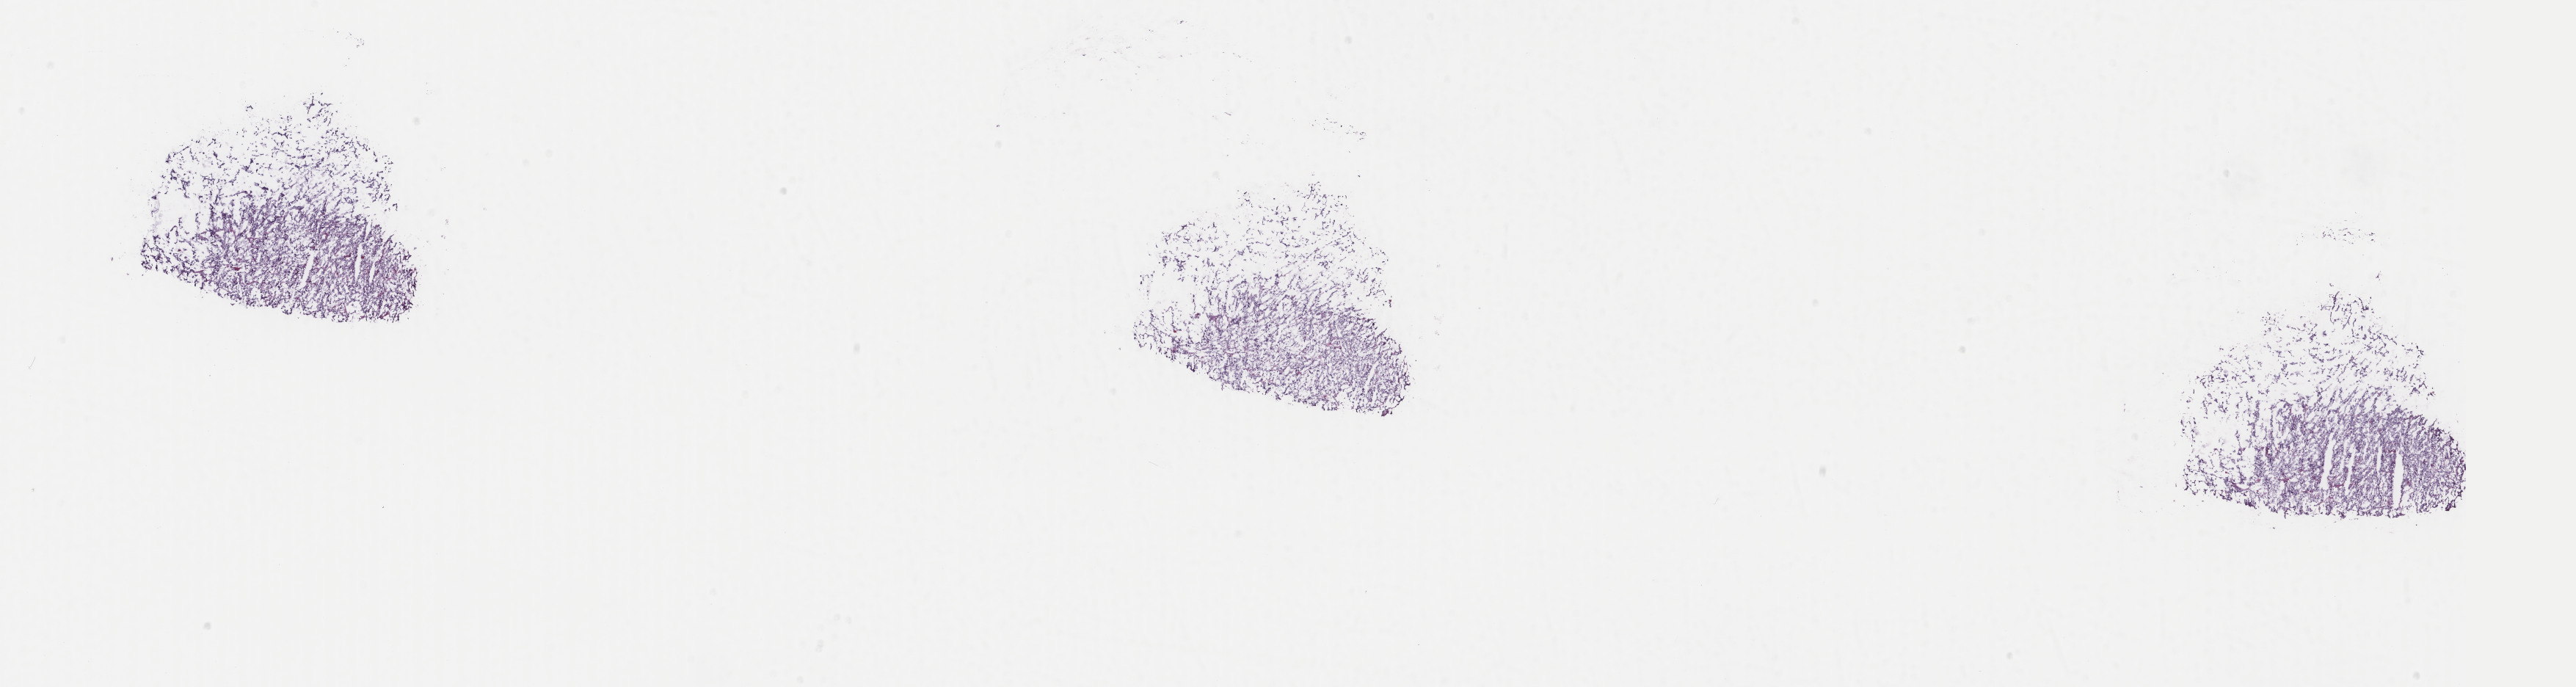
Hematoxylin and eosin (H&E) stained whole-slide image, low-resolution overview of the scanned area, about 27.9 x 7.4 mm (from a 40x scan), frozen section from the top of the tissue portion, adrenal gland, primary tumour sample. Female patient; age at initial diagnosis 21 years. Composition of this section per pathologist review: tumour cells 85%, tumour nuclei 85%, normal cells 0%, stromal cells 15%, necrosis 0%. Infiltration values recorded for this section: lymphocyte infiltration 2%, monocyte infiltration 1%, neutrophil infiltration 1%.
Diagnosis: Pheochromocytoma, malignant. Laterality: left.